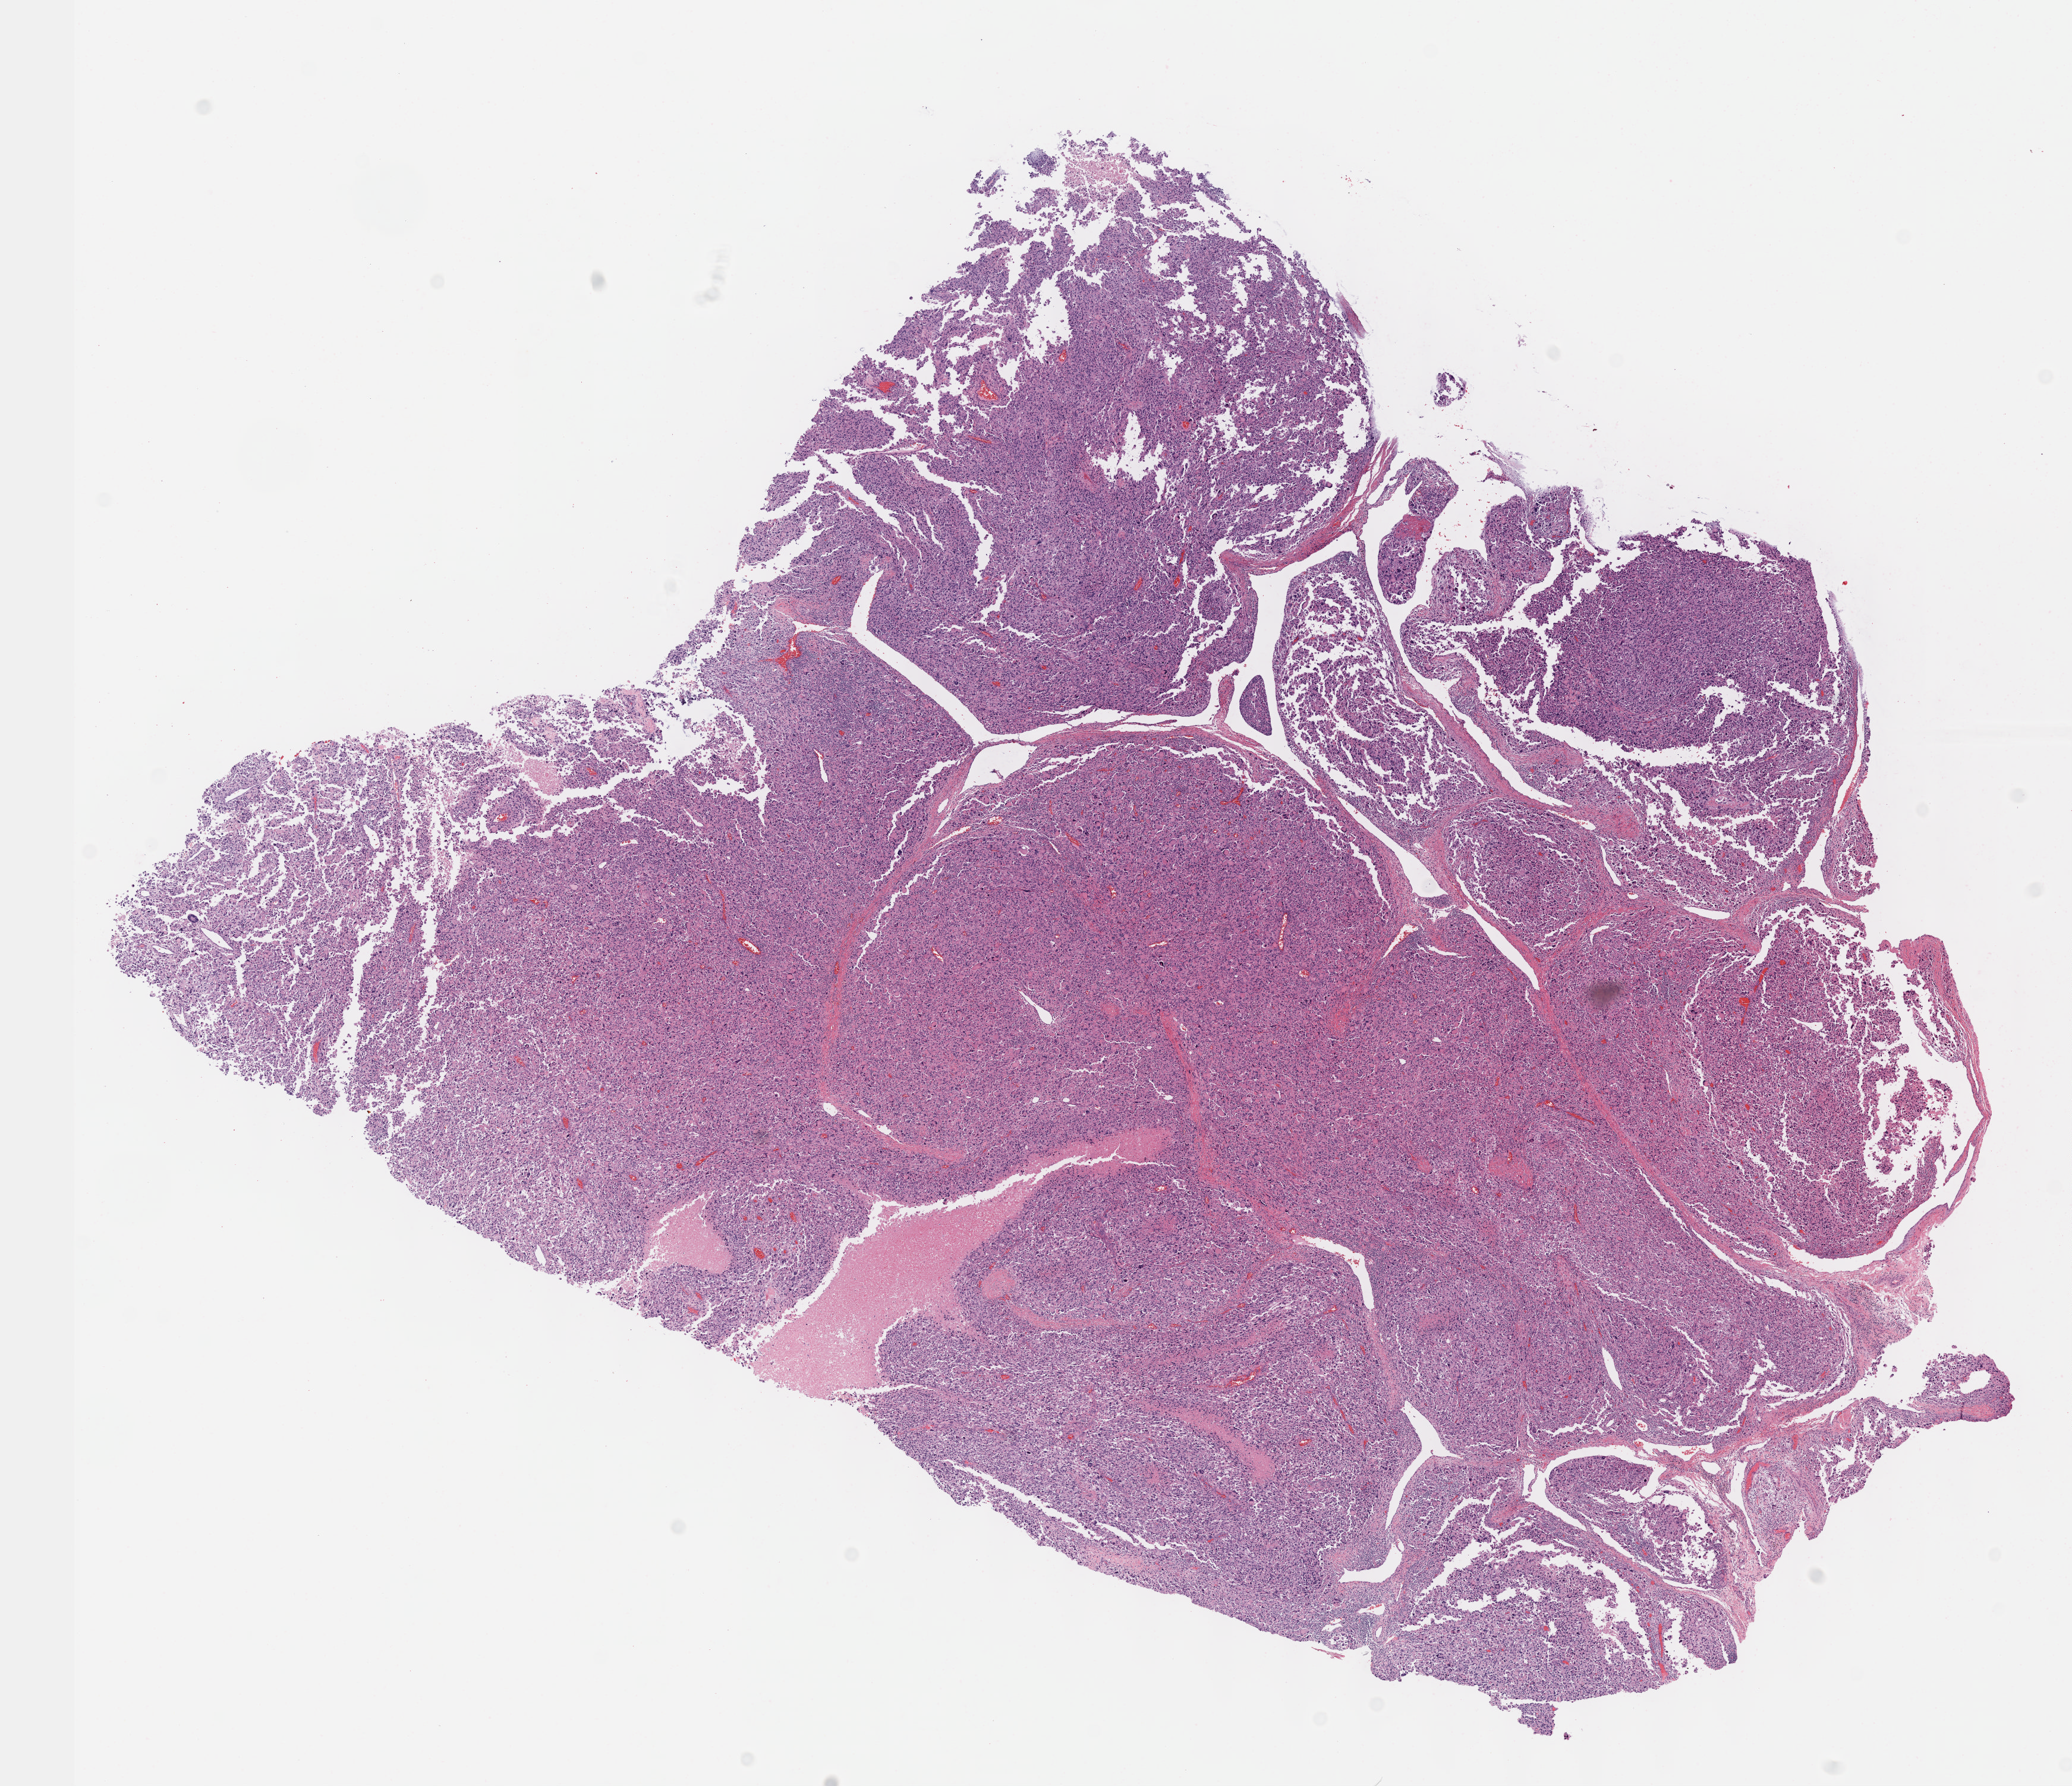
Digitized Hematoxylin and eosin (H&E) stained tissue section (whole slide), shown as a low-resolution overview of the whole scanned area (about 14.1 x 12.1 mm, from a 40x scan); formalin-fixed paraffin-embedded (FFPE) diagnostic section; primary tumour sample from the connective, subcutaneous and other soft tissues. Male patient; age at initial diagnosis 70 years.
Pathologic diagnosis: Leiomyosarcoma, NOS.